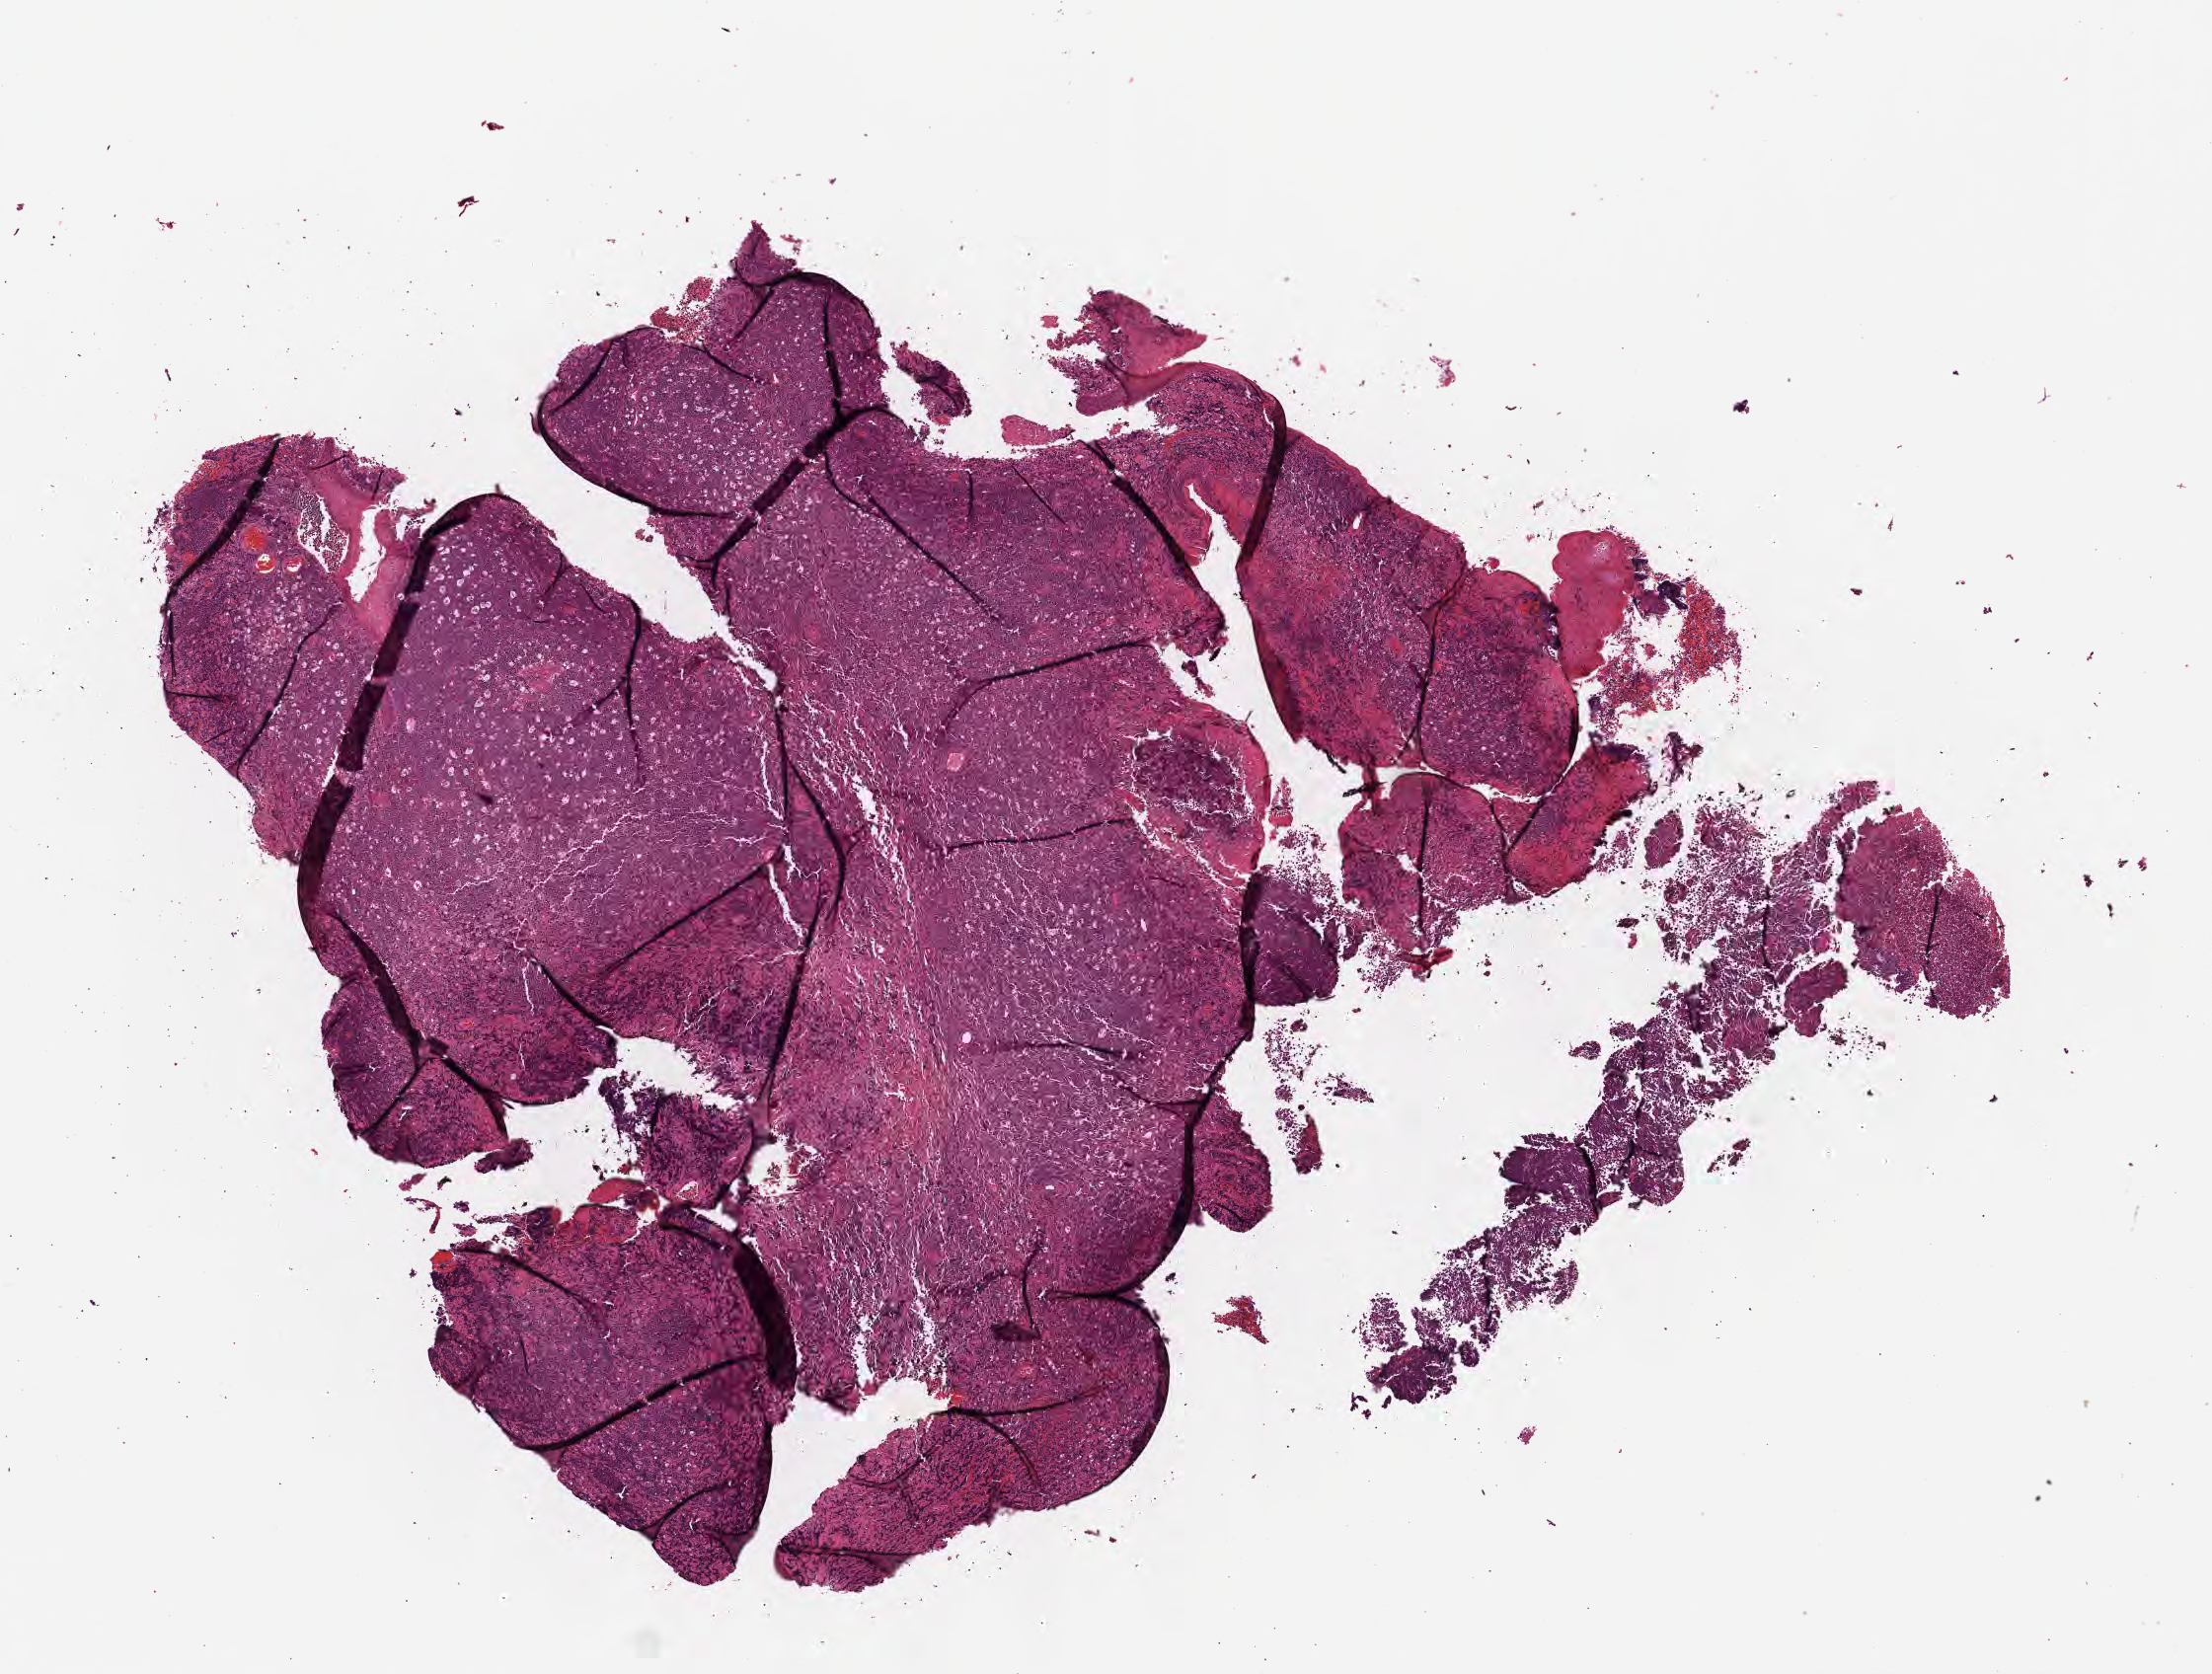
Hematoxylin and eosin (H&E) whole-slide image — whole scanned area (about 9.1 x 6.9 mm) shown as a low-resolution overview, formalin-fixed paraffin-embedded section, primary tumor. Patient: male, age at initial diagnosis 3 years. Composition of this section per pathologist review: tumor cells 95%, tumor nuclei 90%, stromal cells 5%, necrosis 0%, normal cells 0%. Infiltration values recorded for this section: lymphocyte infiltration 80%, monocyte infiltration 10%, neutrophil infiltration 0%.
- histologic diagnosis: Burkitt lymphoma, NOS
- section: top of the tissue portion
- Ann Arbor stage (patient): Stage II